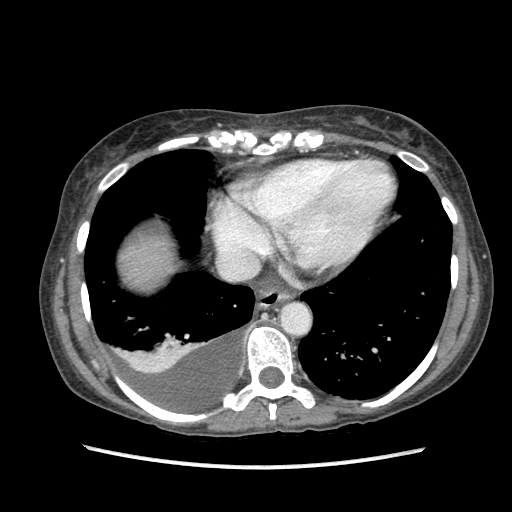
Contrast-enhanced abdominal CT (liver protocol), one axial slice. Position 82 of 87 along the scan axis. Reconstruction kernel STANDARD. 120 kVp. Soft-tissue window (W 400 / L 40 HU). 2.5 mm slice thickness. 512 × 512 image matrix. Case-level facts recorded for this patient, not image findings: diagnosis: hepatocellular carcinoma (patient treated with transarterial chemoembolisation; whether this scan precedes or follows treatment is not stated here); TNM stage (as recorded): Stage-IIIB; Child-Pugh class: A.
Structures marked on this image (semi-automatically segmented with operator editing):
- liver parenchyma outside the tumour (the mass and vessels are separate outlines, so this box may not span the whole liver): box from (x=120, y=236) to (x=172, y=286) px